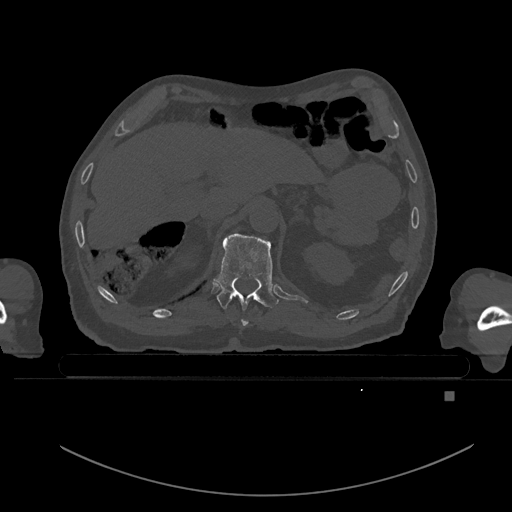
CT including the spine, one axial slice; position 34 of 969 along the scan axis; bone window (W 1800 / L 400 HU); 512 × 512 image matrix. Male patient, age 82 years. From the clinical record (not read from this slice): primary cancer: prostate; vertebrae with lytic lesions (as recorded): T11, T9, T8, T2.
Annotated regions visible in this slice (semi-automatically segmented with operator editing):
- T11 vertebra: bounding box (x1, y1, x2, y2) in pixels: (214, 233, 278, 326)